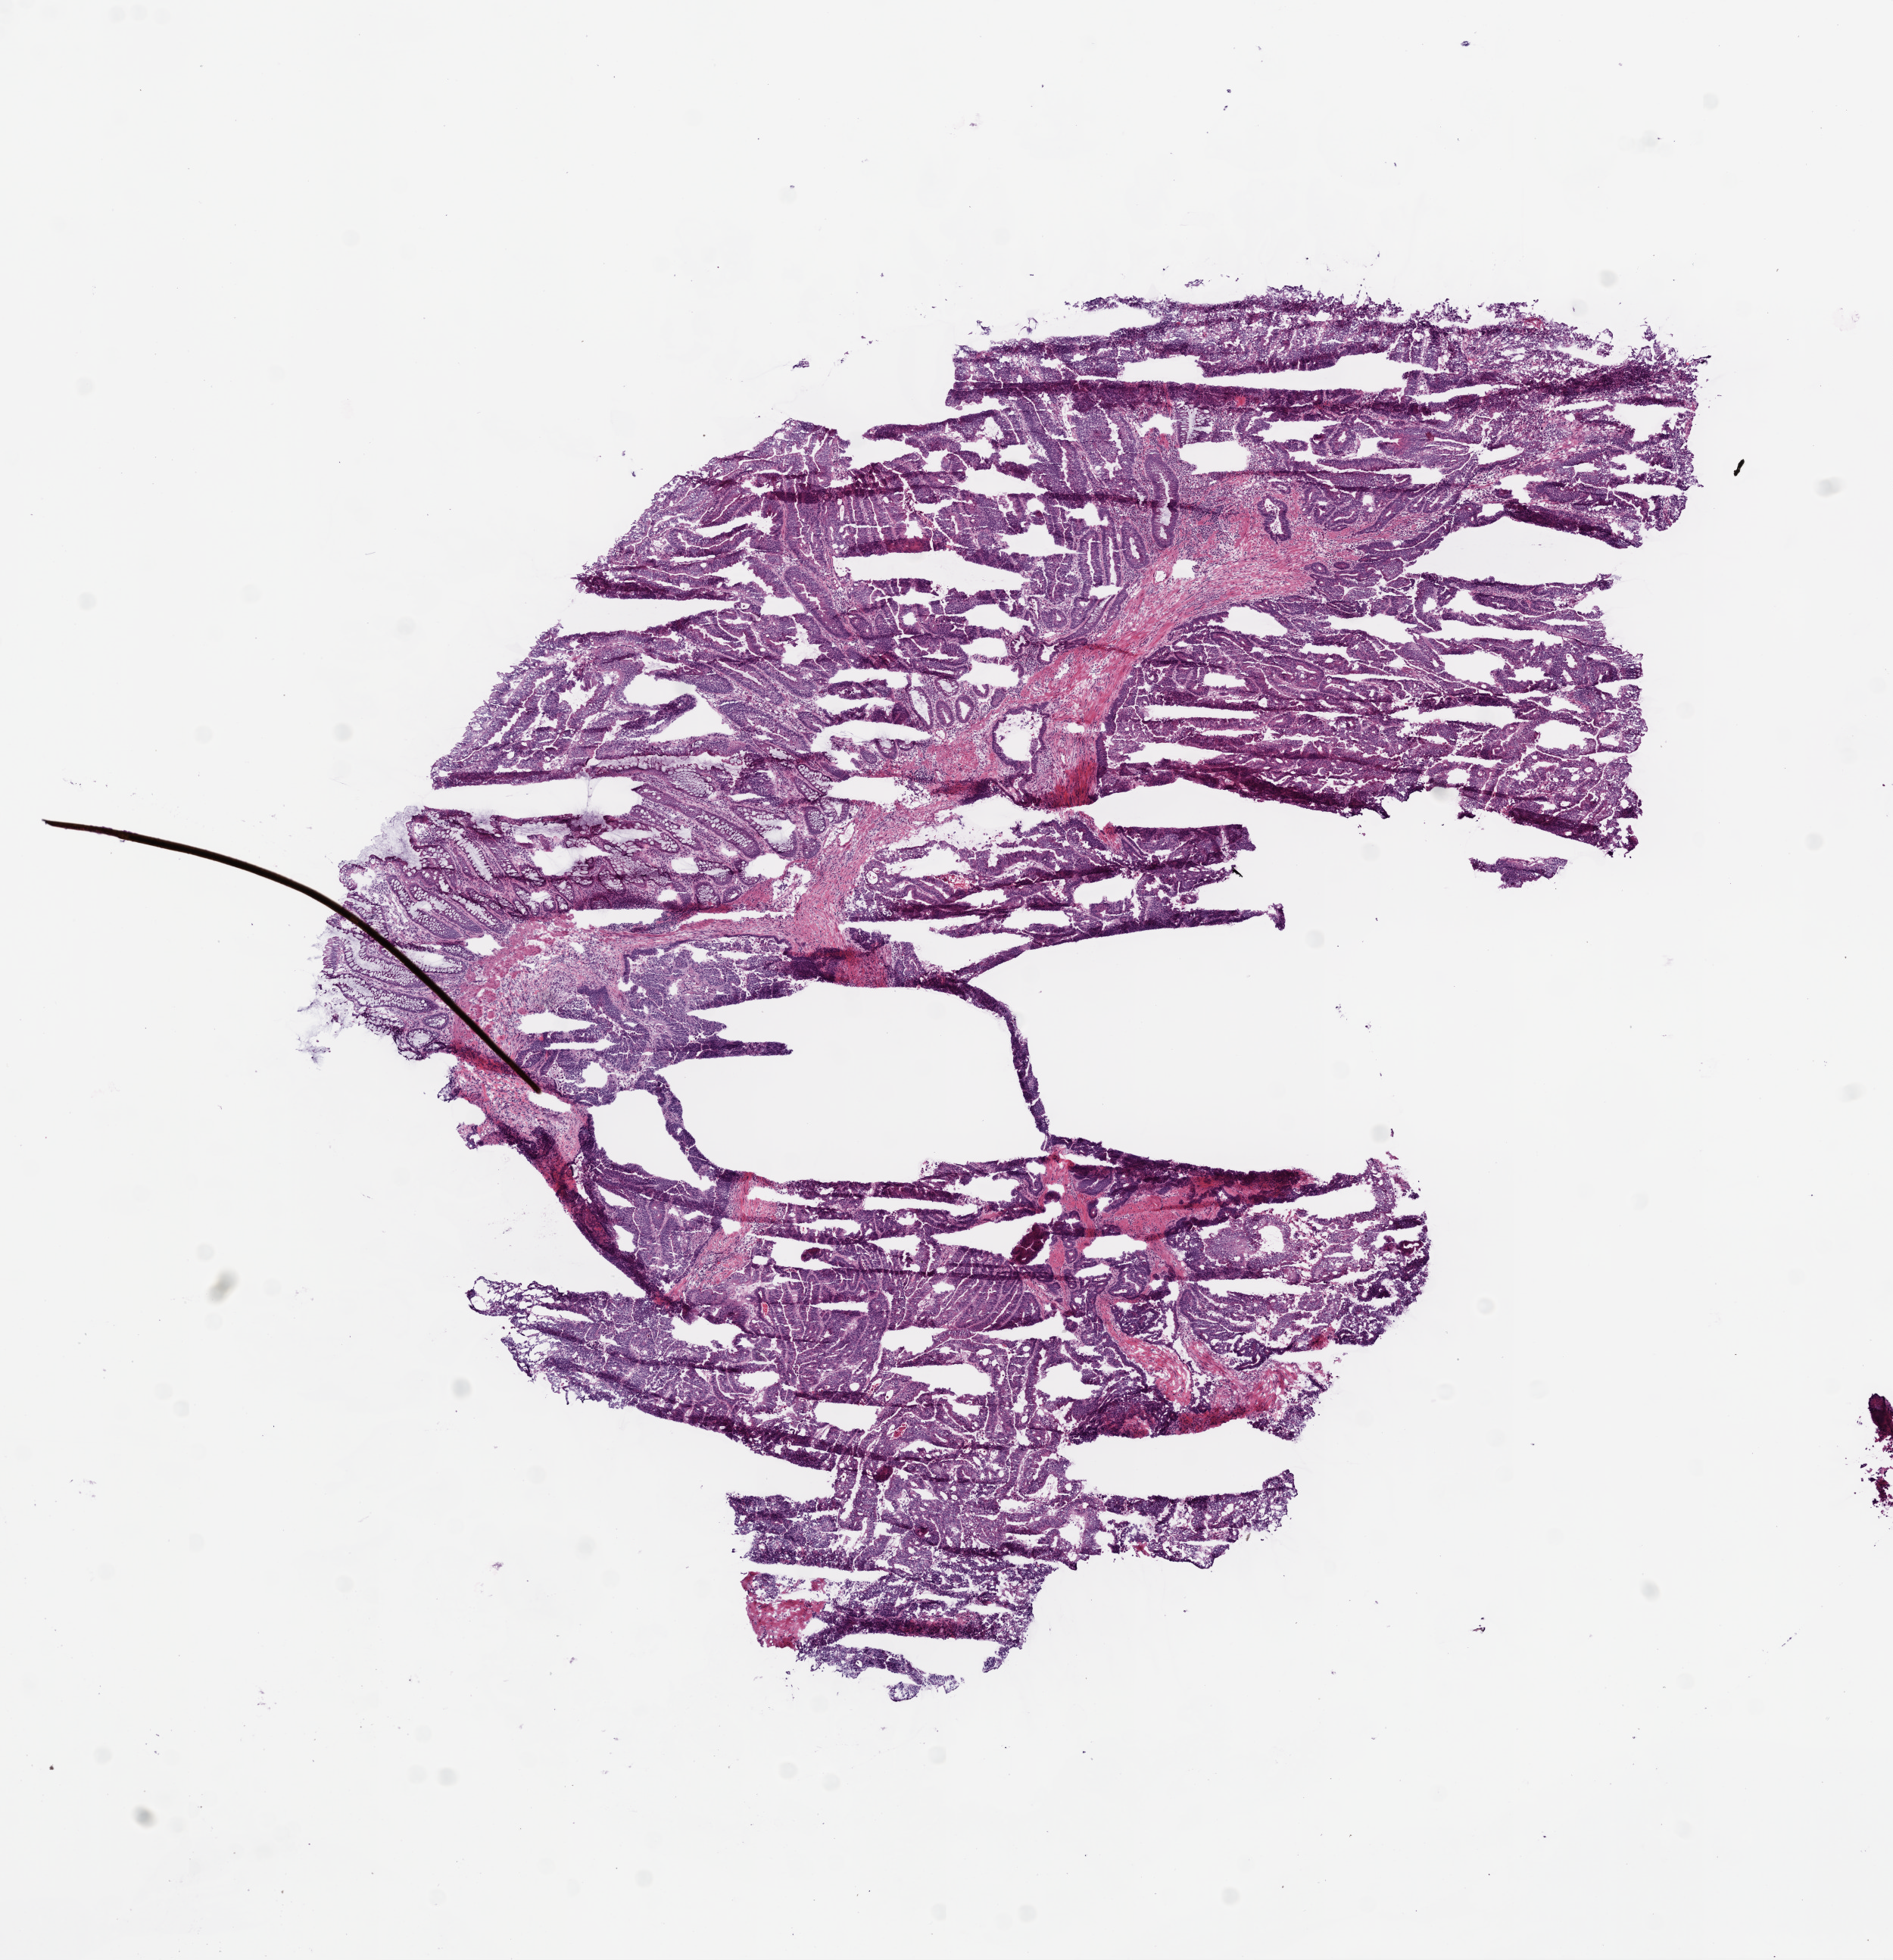
Digitized Hematoxylin and eosin (H&E) stained tissue section (whole slide), whole scanned area (about 10.0 x 10.4 mm) shown as a low-resolution overview. Frozen section from the bottom of the tissue portion. Primary tumour sample from the rectum. Female patient. Composition of this section per pathologist review: tumour cells 84%, tumour nuclei 70%, normal cells 5%, stromal cells 12%, necrosis 1%.
- TNM: T3 N2 M0
- pathologic diagnosis: Adenocarcinoma, NOS
- AJCC pathologic stage: III (5th edition)